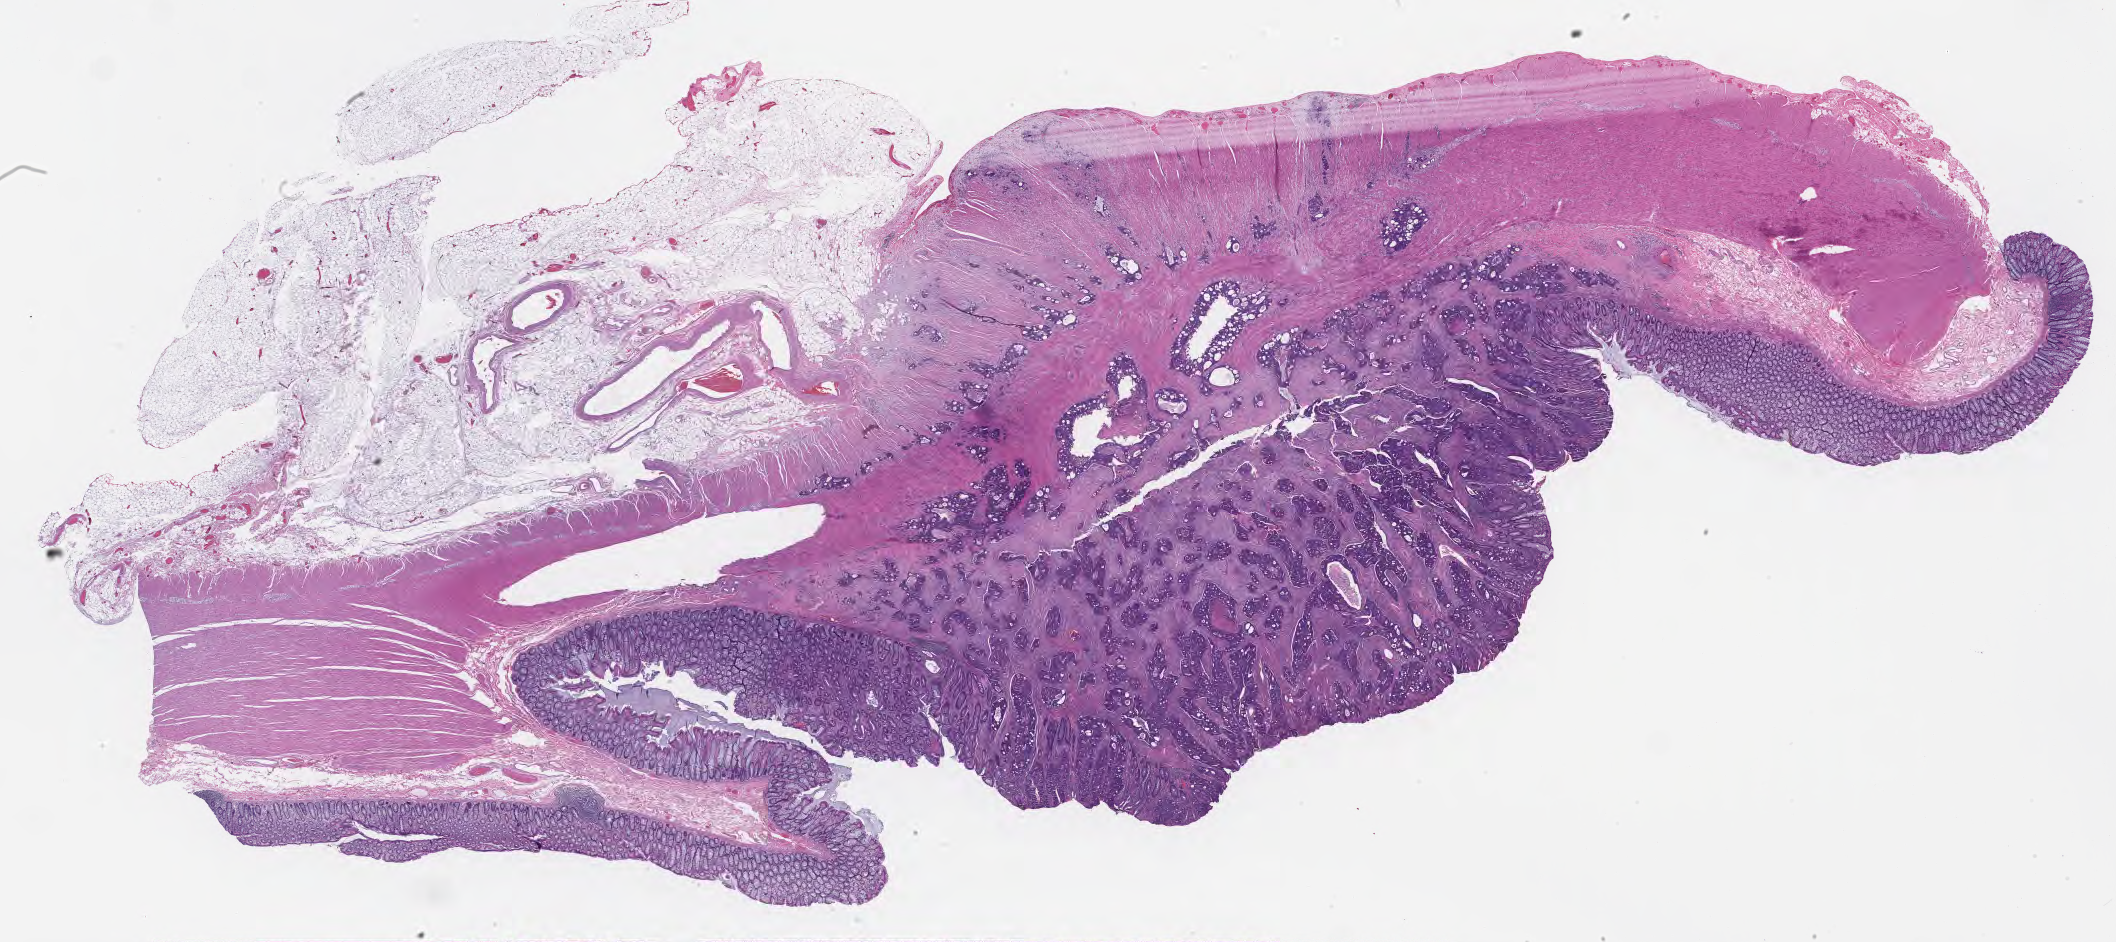
Digitized hematoxylin and eosin (H&E)-stained section — low-resolution overview of the scanned area, about 34.1 x 15.2 mm; formalin-fixed, paraffin-embedded (FFPE) tissue; primary tumor; site: sigmoid colon. Patient: female, age at initial diagnosis 47 years.
Diagnosis: Adenocarcinoma, intestinal type.